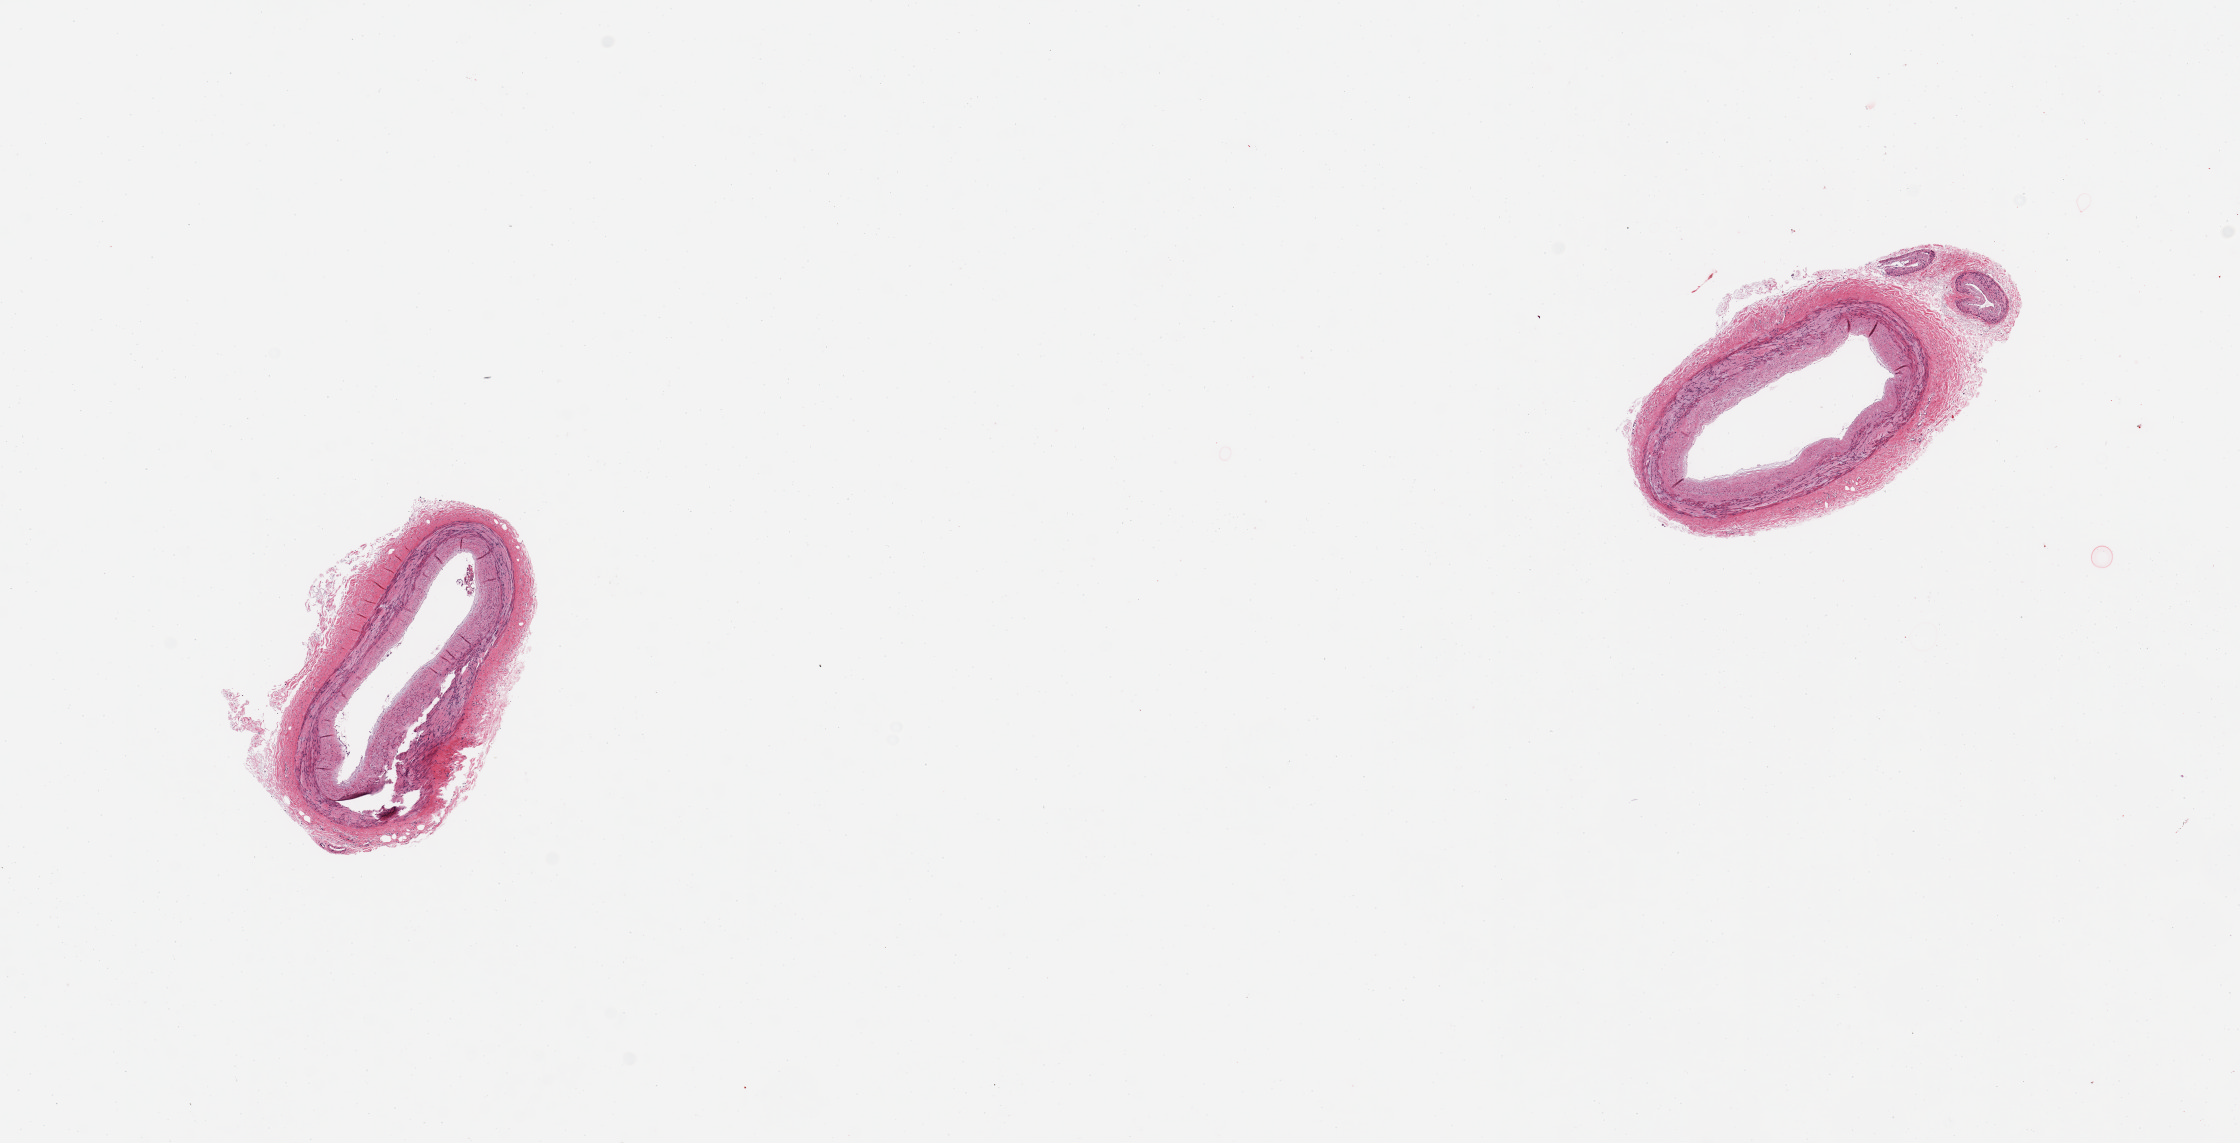
Hematoxylin and eosin (H&E) whole-slide image, low-resolution overview of the scanned area, about 17.7 x 9.0 mm. PAXgene-fixed paraffin-embedded (PFPE) section. Section of tibial artery (target tissue). Tissue donor sample. Female donor.
- reviewer comment on this tissue sample: 2 pieces, minimal adherent fat/atherosis